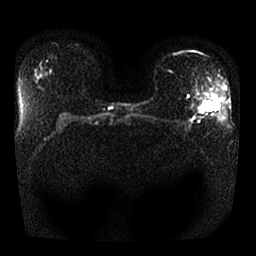
Breast MRI, one axial slice. Position 15 of 25 along the scan axis. Diffusion-weighted series; image 2 of 4 stored at this slice position (different b-values; order by instance number). 1.5 T. 4 mm slice thickness. 256 × 256 image matrix, field of view 340 × 340 mm. Female patient.
Outlined on this slice (manually delineated by an expert):
- tumour on diffusion-weighted imaging: bounding box [x1, y1, x2, y2] px = [200, 102, 217, 112]